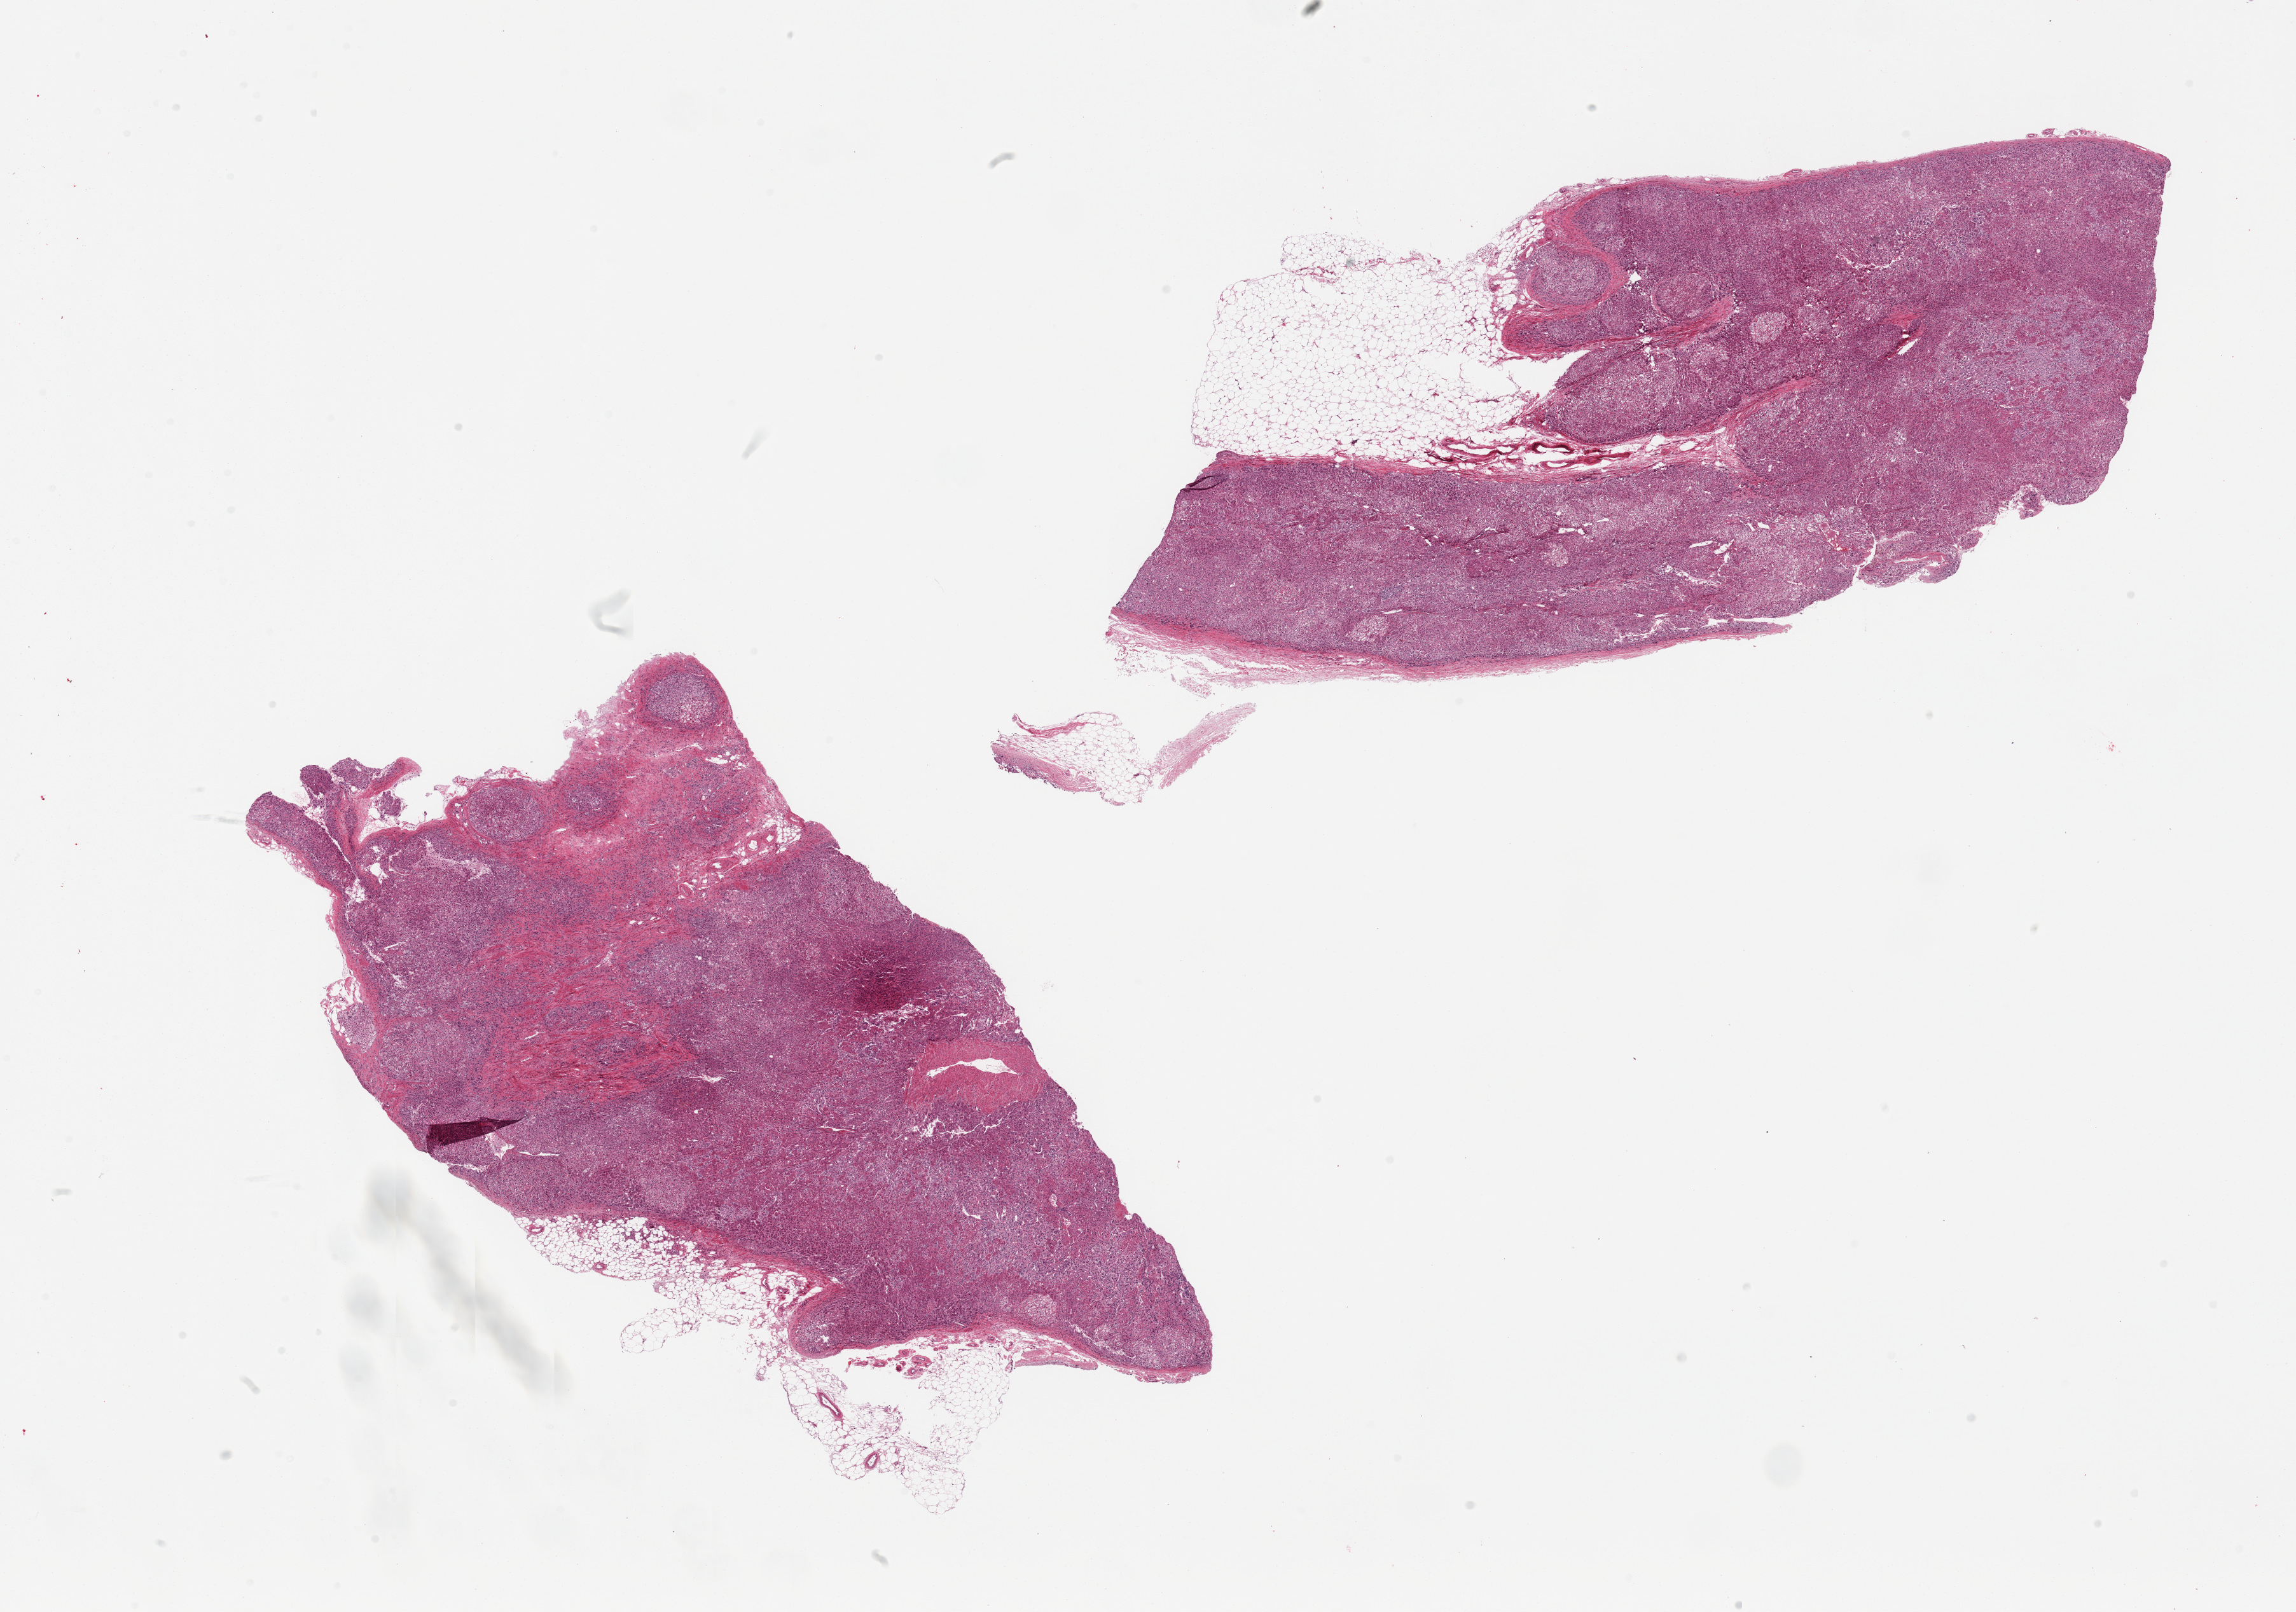
Whole-slide image, H&E stain — low-resolution overview of the scanned area, about 28.5 x 20.0 mm (from a 20x scan), PAXgene-fixed, paraffin-embedded tissue, target tissue: adrenal gland, tissue donor sample. Donor: female.
Pathologist's review note for this sample: 2 pieces; 10 & 30% external fat.